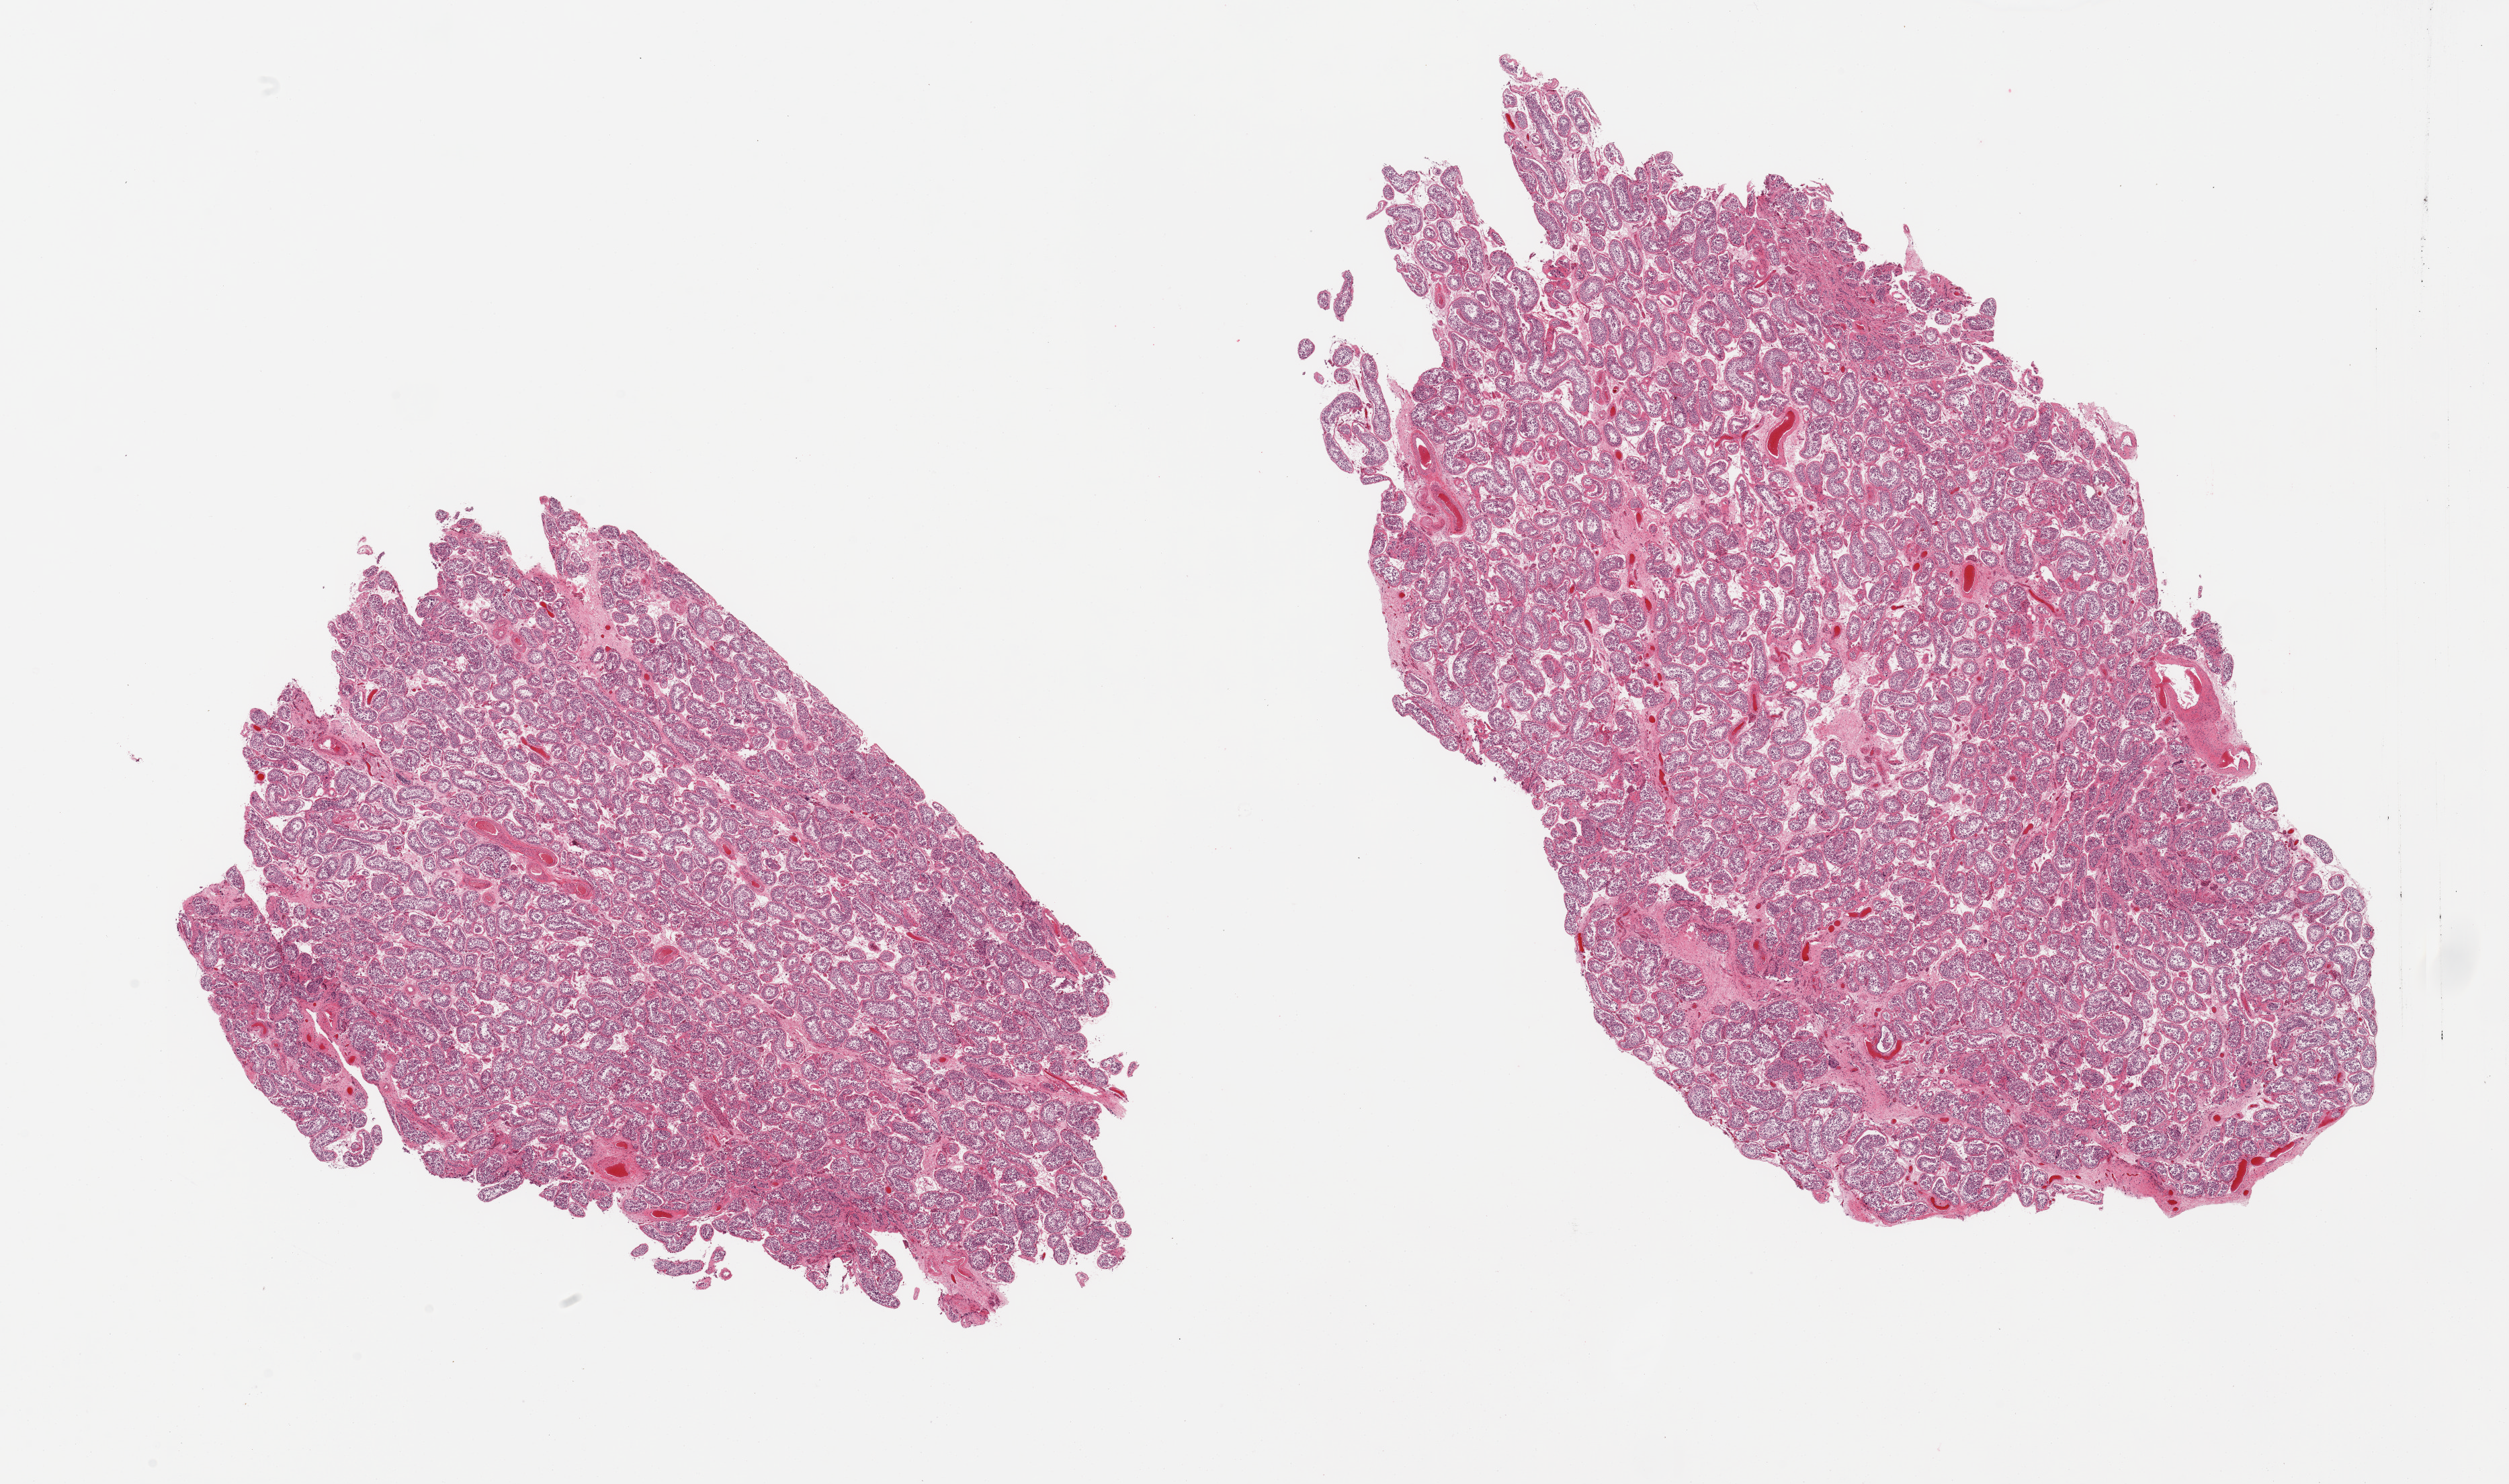
Digitized H&E-stained section, a low-resolution overview of the entire scanned area, about 29.5 x 17.5 mm, PAXgene-fixed, paraffin-embedded tissue, target tissue: testis, tissue donor sample.
* review note (as recorded): 2 pieces; oversized, spermatogenesis is present